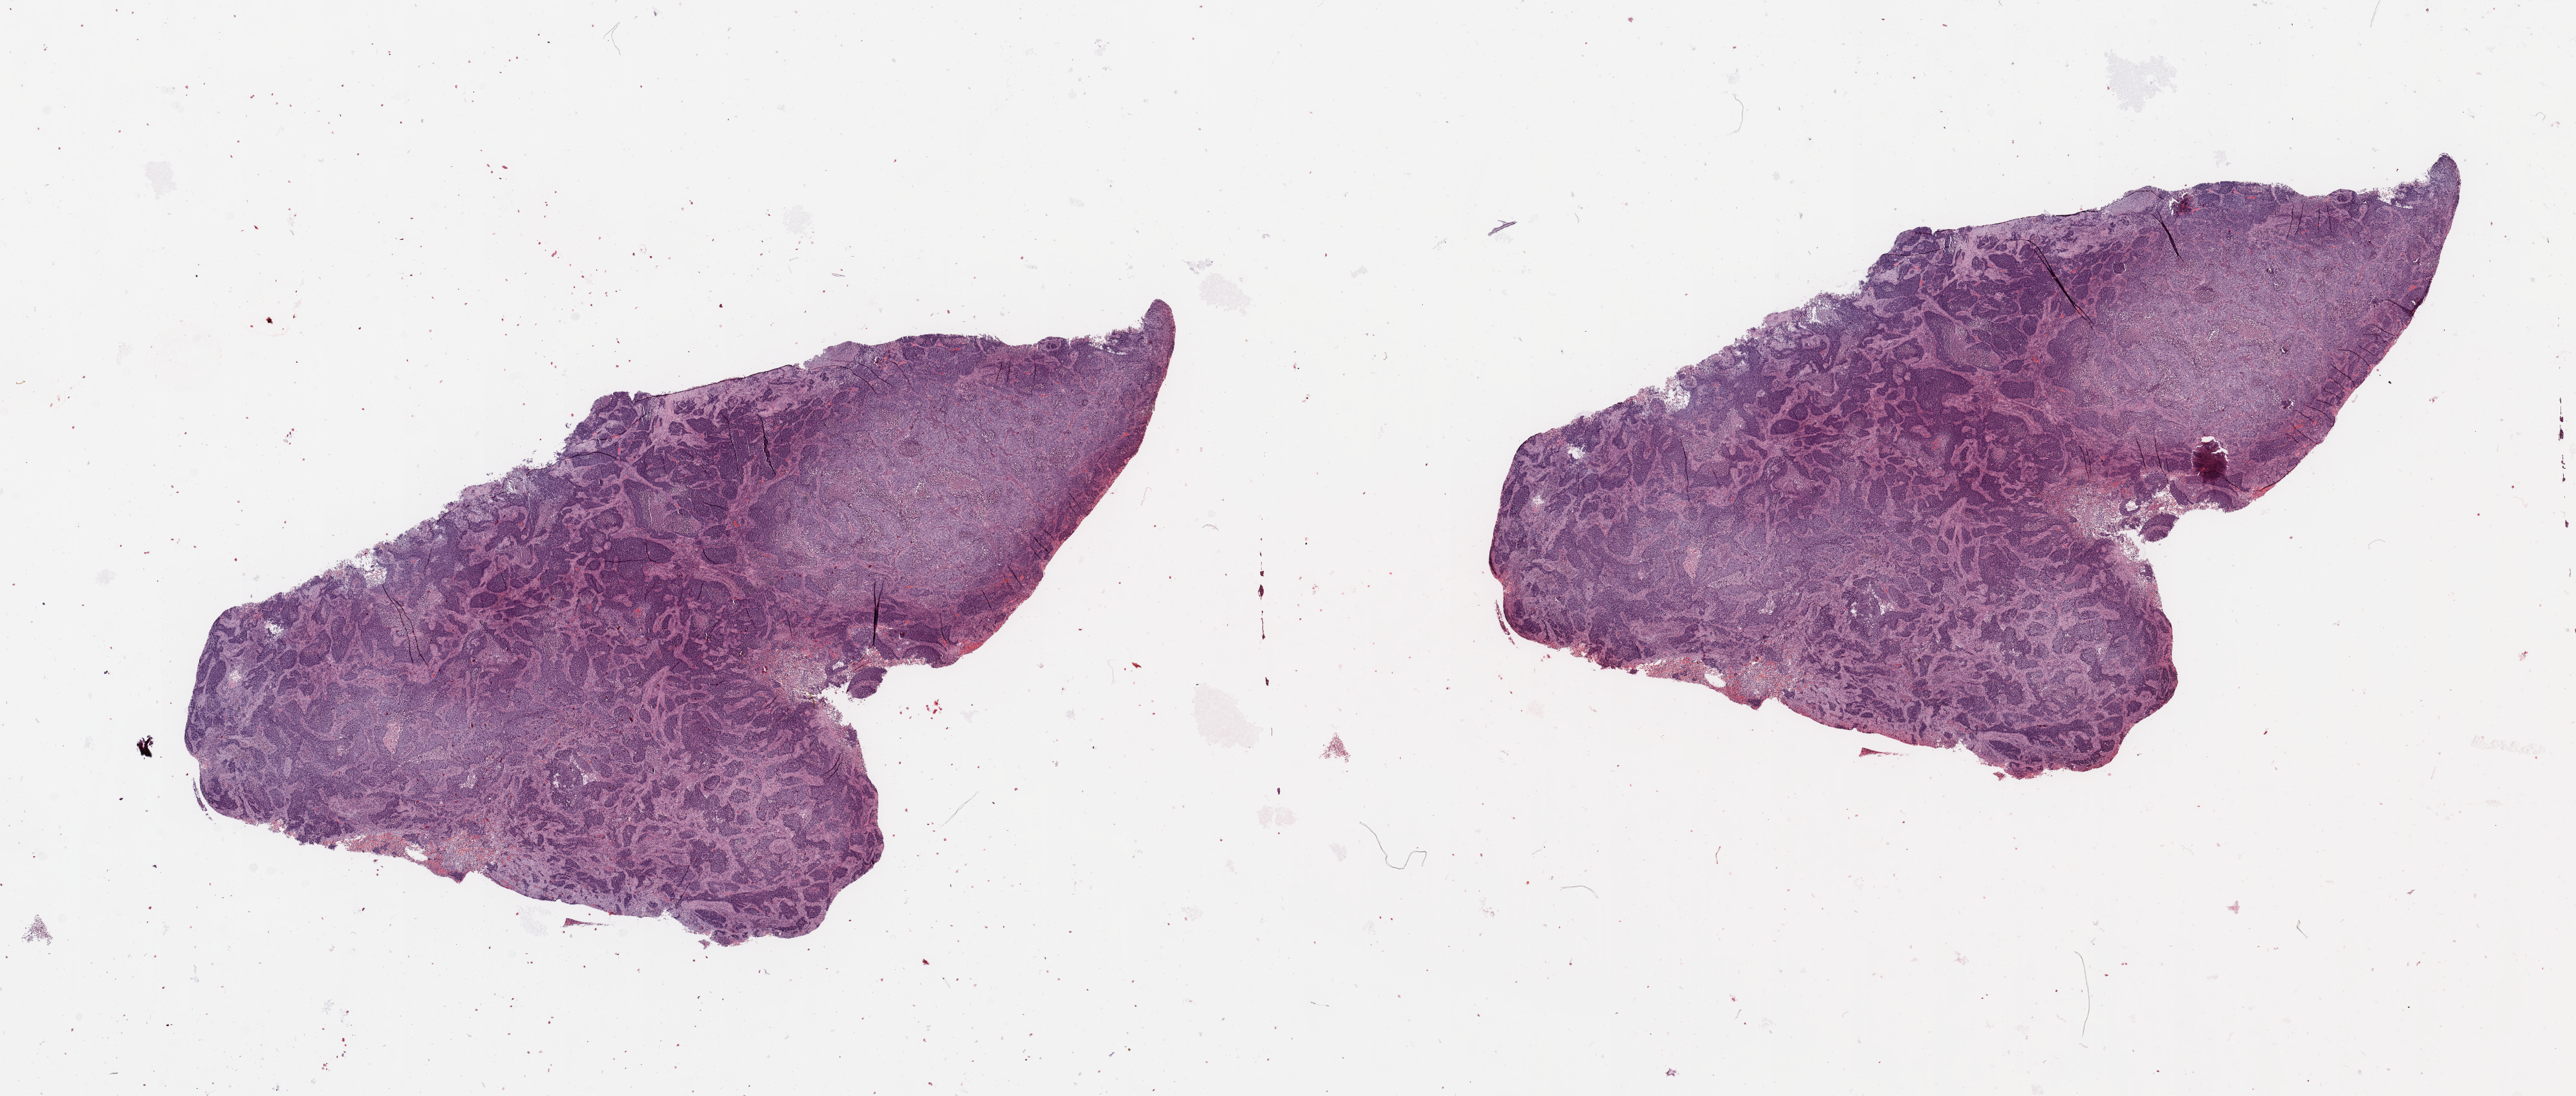
Hematoxylin and eosin (H&E) stained whole-slide image, low-resolution overview of the scanned area, about 31.5 x 13.4 mm (from a 20x scan), lung, tumour tissue. Patient: male, age 73 years.
Diagnosis: Squamous cell carcinoma, NOS.